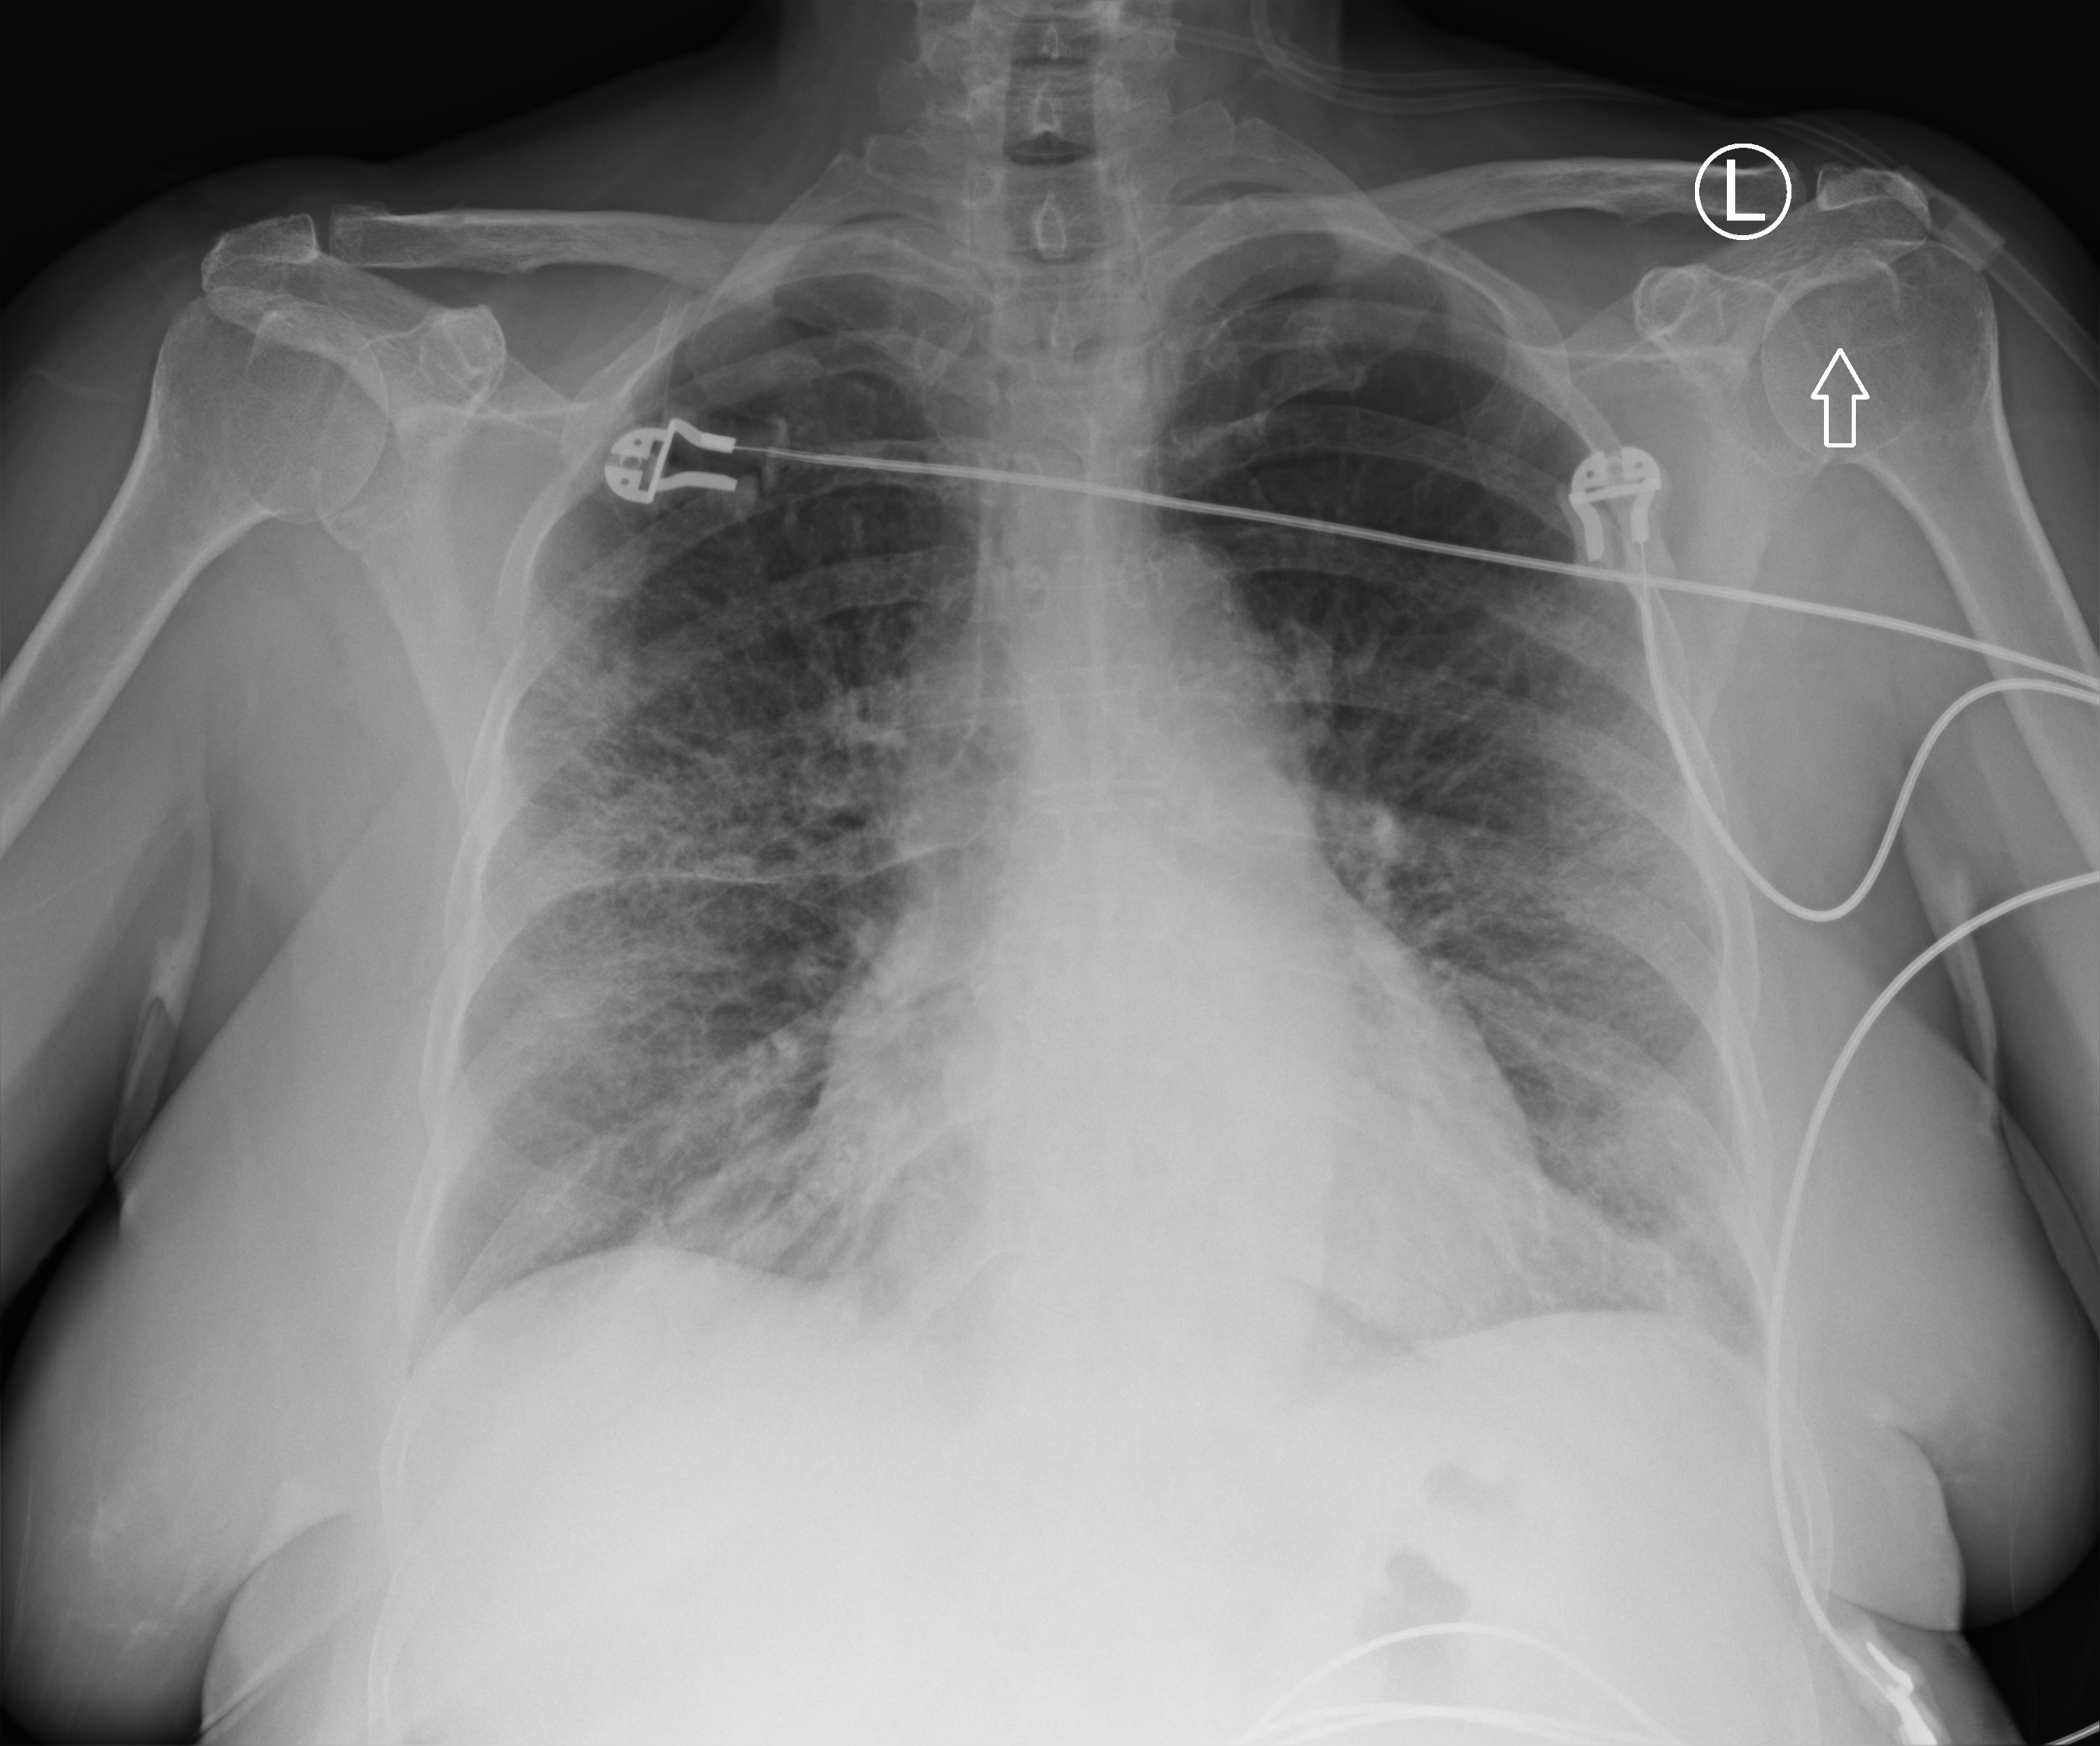
Portable chest radiograph; anteroposterior (AP) projection. Female patient hospitalised with COVID-19, age 60–74 years.
Hospital-stay facts (about this admission, not read from this image; timing relative to this image not recorded): mechanically ventilated during this hospital stay: yes; admitted to intensive care during this hospital stay: yes; chronic kidney disease (admission record): no.